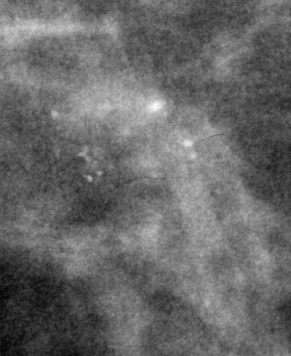
Region of interest cut from a scanned film mammogram (one marked finding); left breast; CC view.
- Calcifications, morphology pleomorphic, distribution clustered; BI-RADS assessment category 4; pathology result (as recorded, not read from the image): malignant.